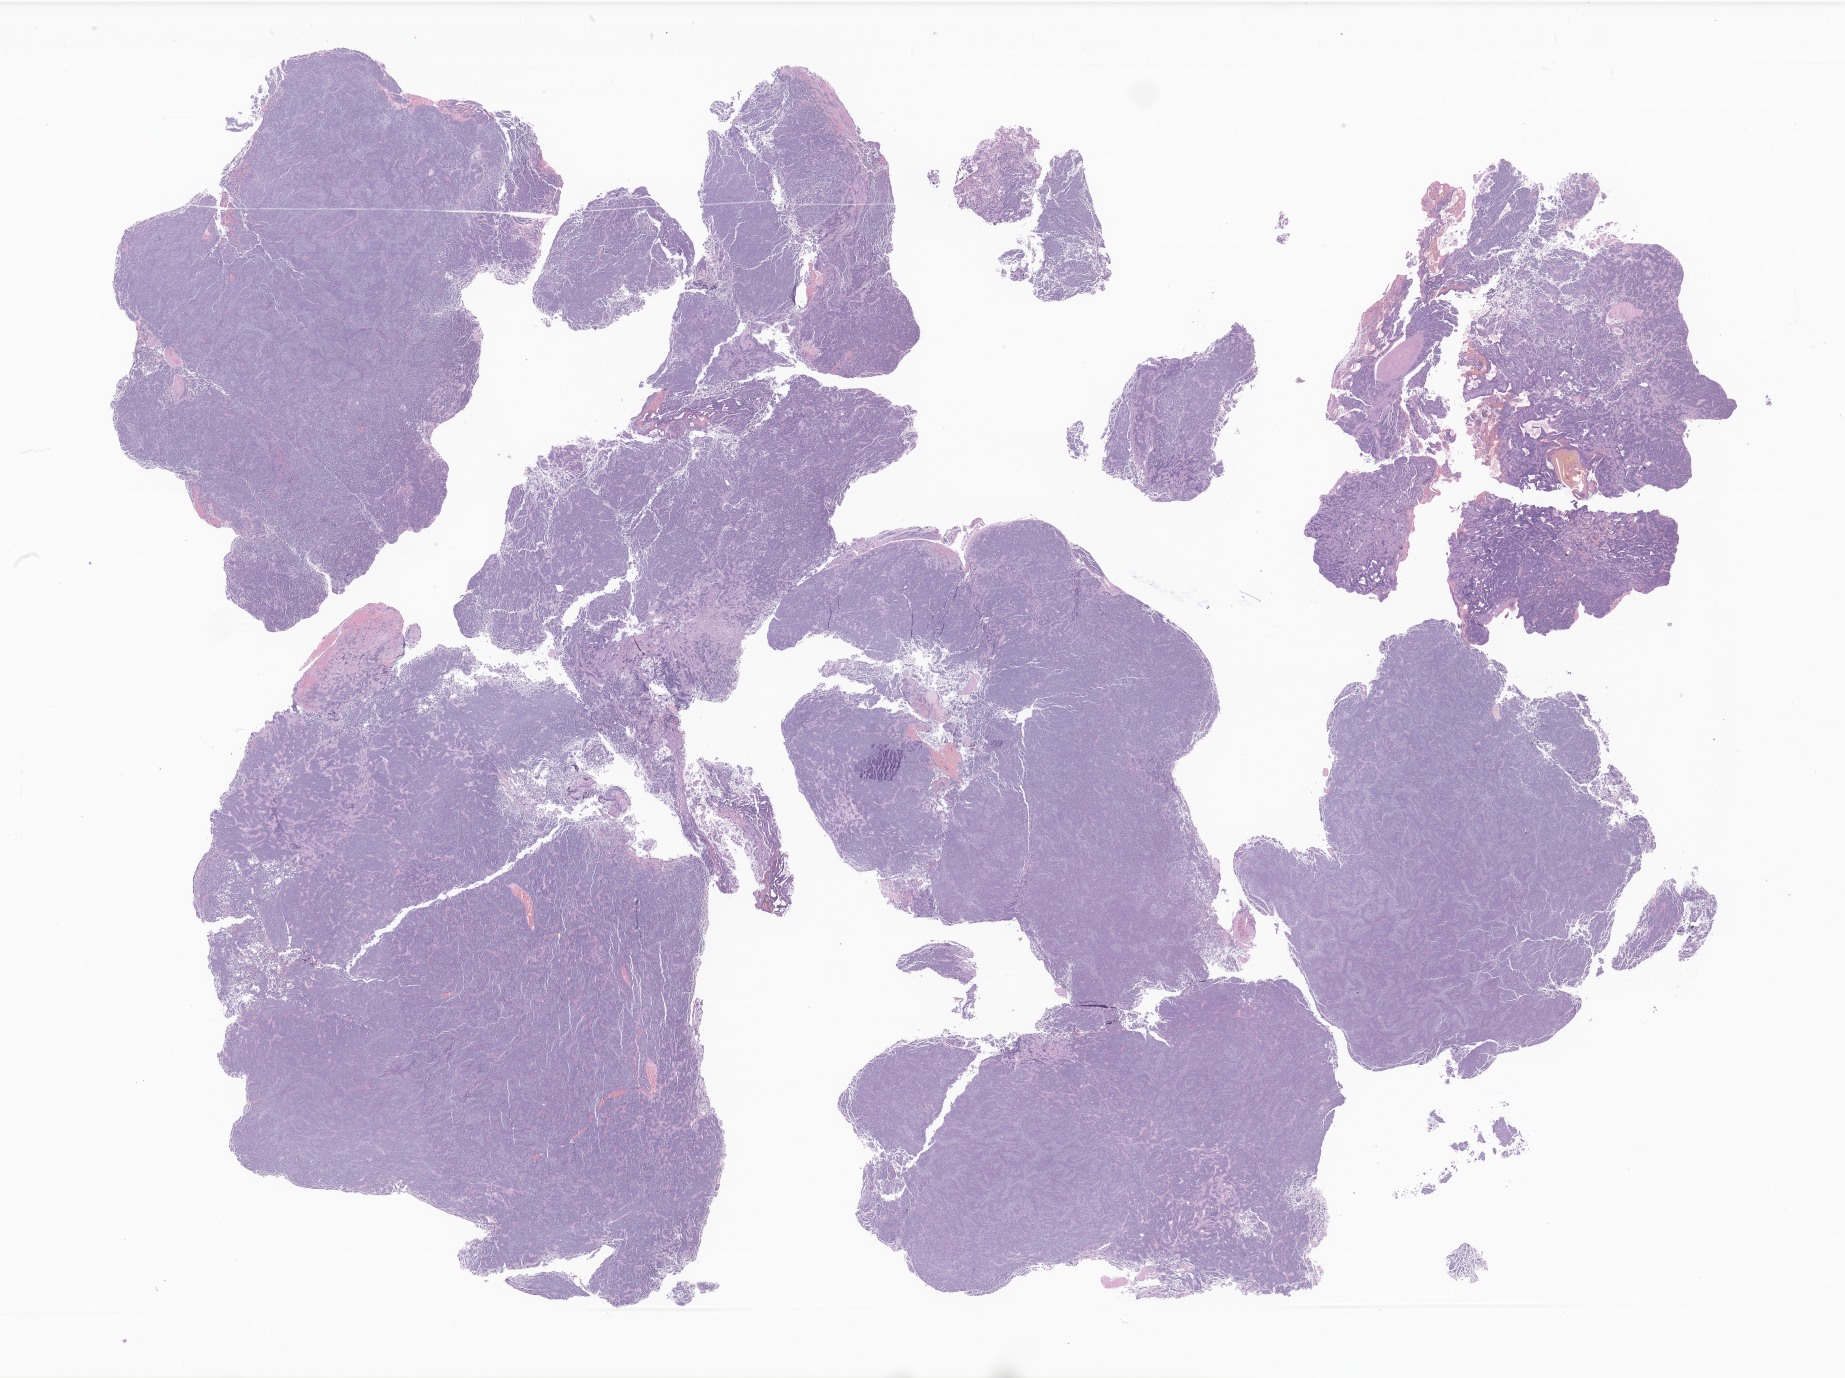
Whole-slide image, haematoxylin and eosin stain of tumor tissue from the cerebellum — low-resolution overview of the scanned area, about 31.1 x 23.2 mm; formalin-fixed, paraffin-embedded (FFPE) tissue. Patient male; age 159 months (13 years 3 months).
Diagnosis (ICD-O-3 morphology term): Desmoplastic nodular medulloblastoma.